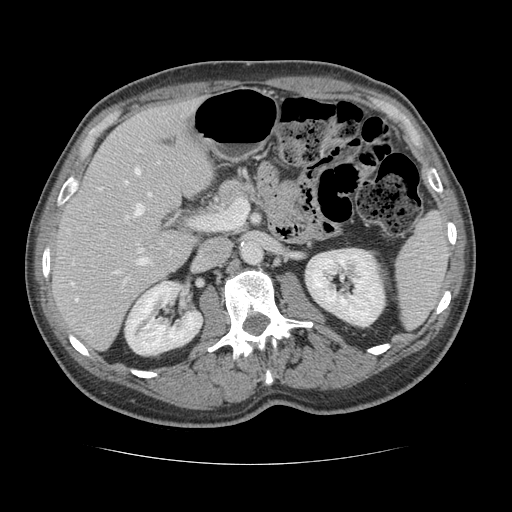
Contrast-enhanced abdominal CT, one axial slice; position 70 of 134 along the scan axis; reconstruction kernel STANDARD; 120 kVp; intravenous contrast given; soft-tissue window (W 400 / L 40 HU); 512 × 512 image matrix, field of view 377 × 377 mm. Male patient, age 68 years. From the clinical record (not read from this slice): diagnosis: colorectal cancer liver metastases, imaged before liver resection; multiple liver metastases: yes.
Annotated regions visible in this slice (outlined manually by an expert reader):
- hepatic veins: bounding box [x1, y1, x2, y2] px = [71, 168, 151, 301]
- liver: [53, 100, 214, 349]
- planned liver remnant (the part of the liver to remain after resection): [53, 100, 214, 337]
- portal vein (with intrahepatic branches): [115, 216, 148, 283]